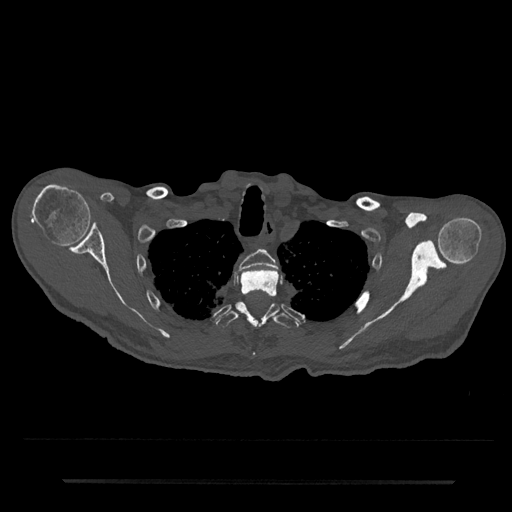
CT including the spine, one axial slice. Position 649 of 797 along the scan axis. Reconstruction kernel Br40s/3. 120 kVp. Bone window (W 1800 / L 400 HU). 0.5 mm slice thickness. 512 × 512 image matrix, field of view 427 × 427 mm. Male patient, age 74 years. Case-level facts recorded for this patient, not image findings: primary cancer: prostate.
Outlined on this slice (semi-automatic segmentation, software-assisted and operator-edited):
- T2 vertebra: bounding box (x1, y1, x2, y2) in pixels: (239, 249, 277, 271)
- T3 vertebra: (240, 269, 279, 298)
- T4 vertebra: (216, 301, 299, 329)